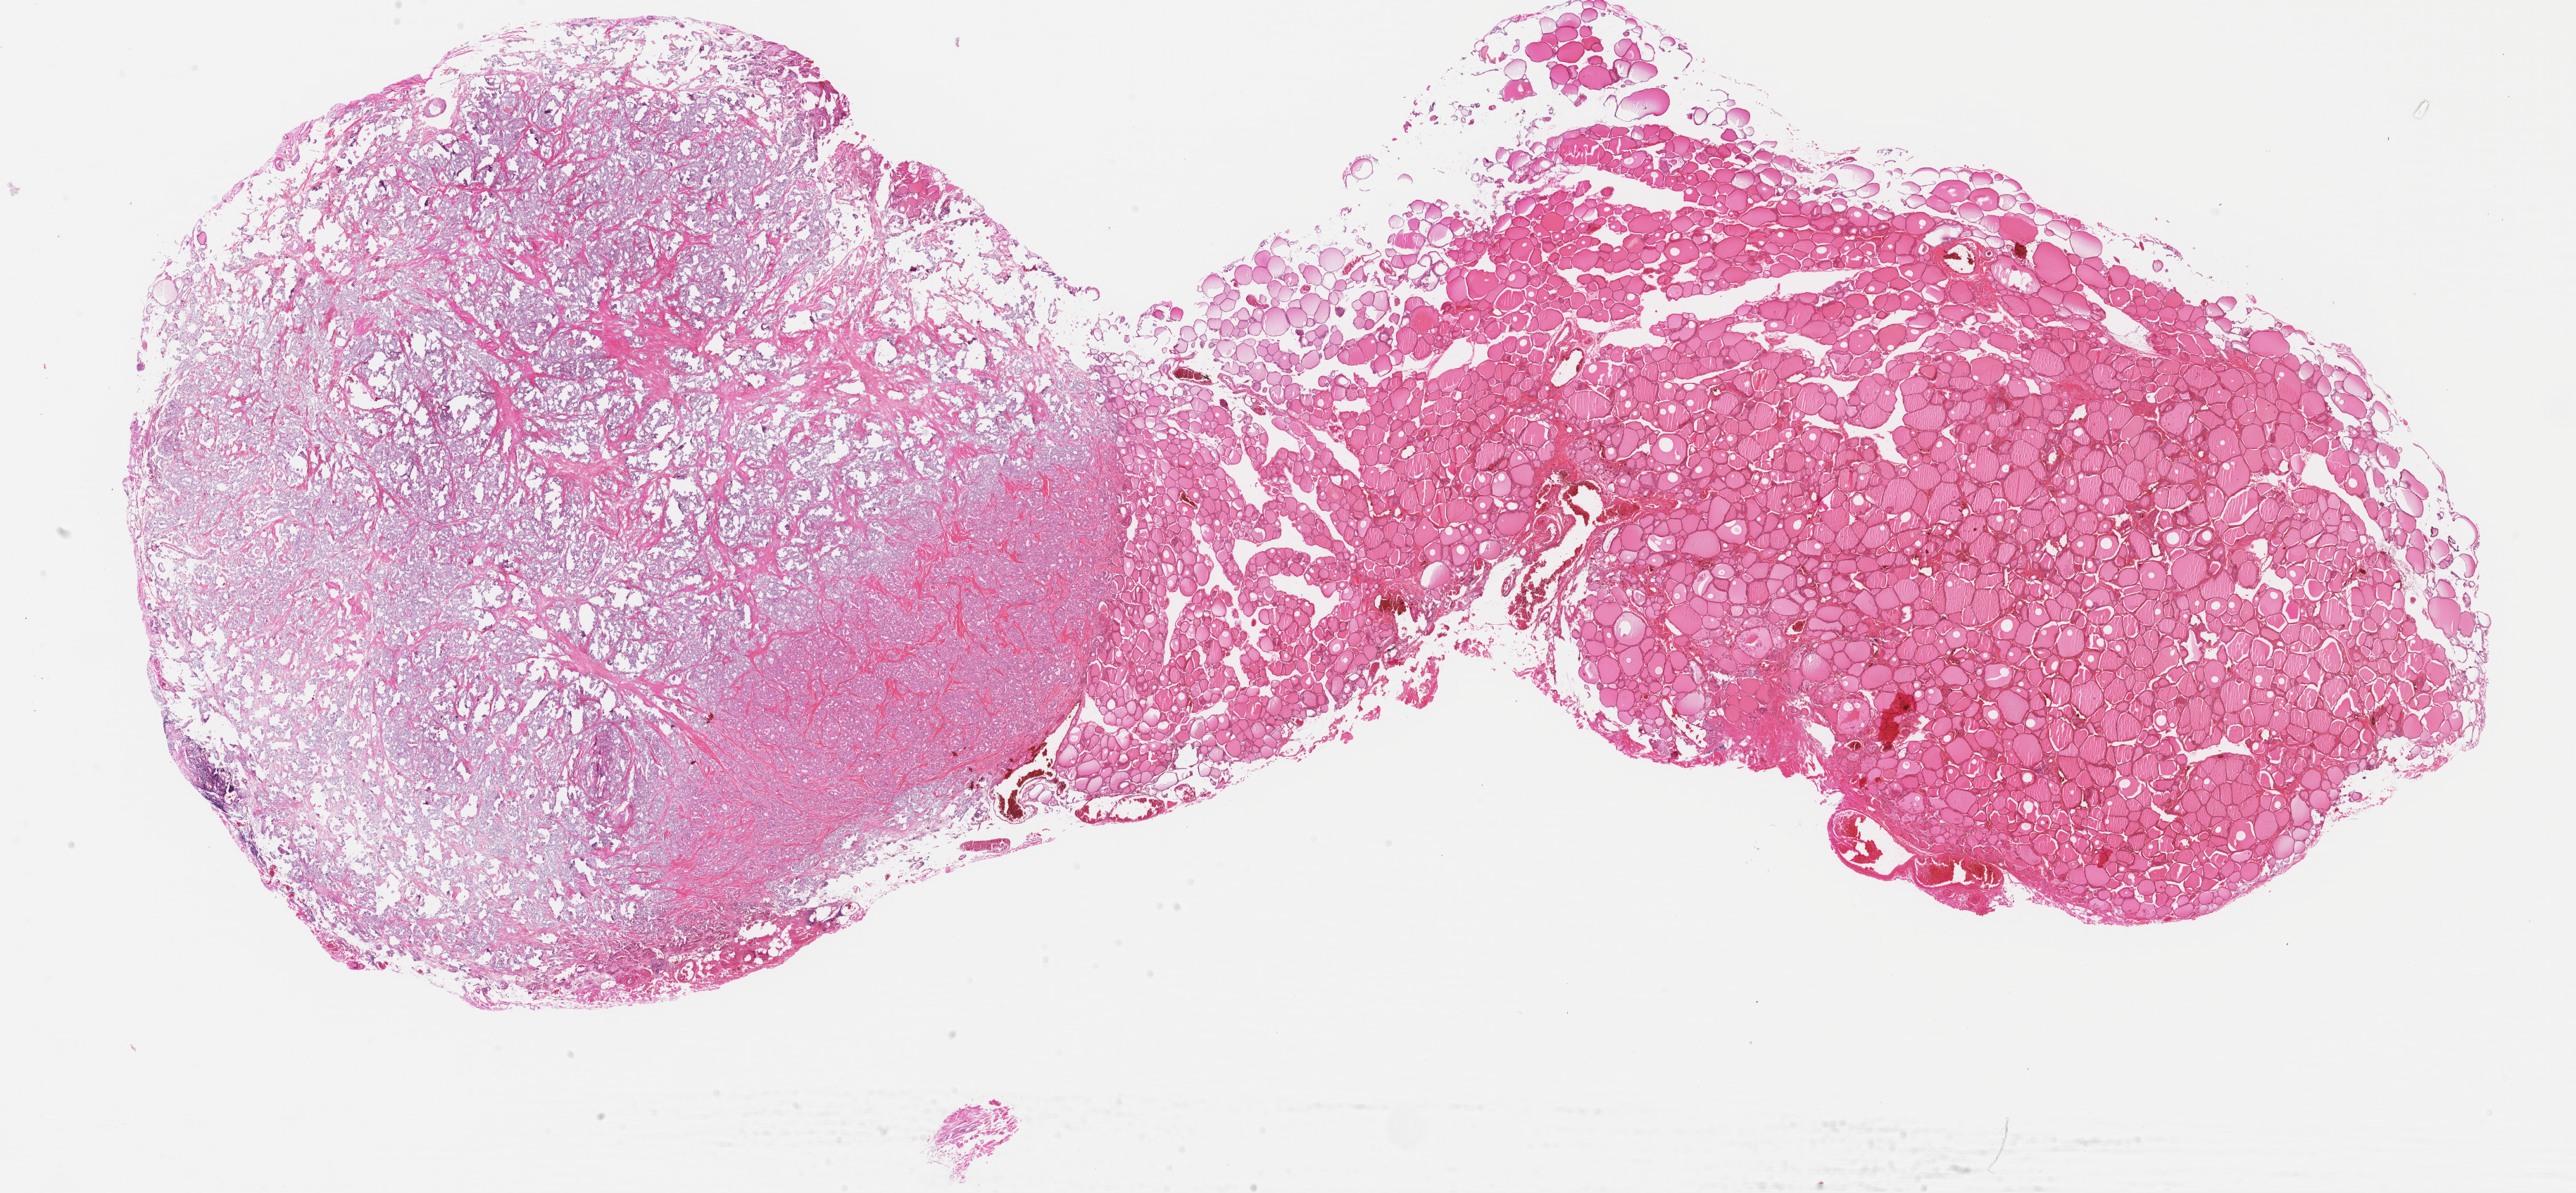
Hematoxylin and eosin (H&E) stained whole-slide image, a low-resolution overview of the entire scanned area, about 28.9 x 13.4 mm (slide scanned at 40x). Formalin-fixed paraffin-embedded (FFPE) diagnostic section. Sample: primary tumour, thyroid. Patient: female, age at initial diagnosis 50 years.
Histologic diagnosis: Papillary carcinoma, follicular variant (thyroid gland).